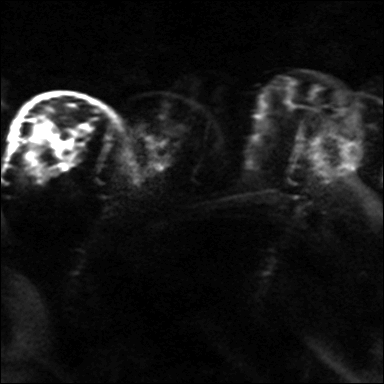
Breast MRI, one axial slice. Position 22 of 36 along the scan axis. Diffusion-weighted series; image 2 of 4 stored at this slice position (different b-values; order by instance number). 3 T. 4 mm slice thickness. 384 × 384 image matrix. Female patient.
Outlined on this slice (expert manual segmentation):
- tumour on diffusion-weighted imaging: bounding box (x1, y1, x2, y2) in pixels: (67, 128, 85, 145)